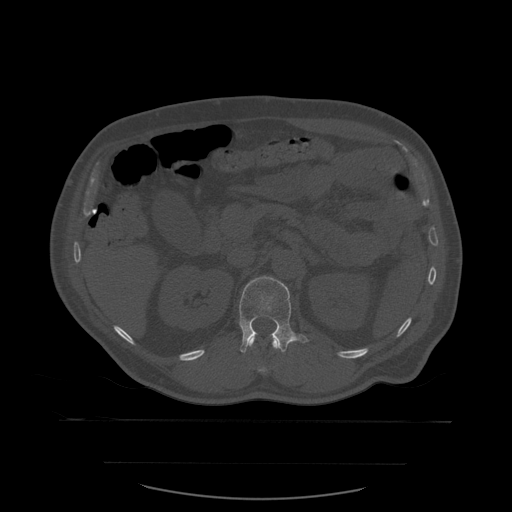
CT including the spine, one axial slice. Slice 252 of 590 in the series (ordered by position). Bone window (W 1800 / L 400 HU). 1.25 mm slice thickness. 512 × 512 image matrix. Patient age 71 years. From the clinical record (not read from this slice): primary cancer: lung; vertebrae with lytic lesions (as recorded): T1, T2, L5, S1.
Annotated regions visible in this slice (semi-automatically segmented with operator editing):
- L1 vertebra: bounding box <239,276,309,354> (left, top, right, bottom; pixels)
- T12 vertebra: <241,338,287,372>